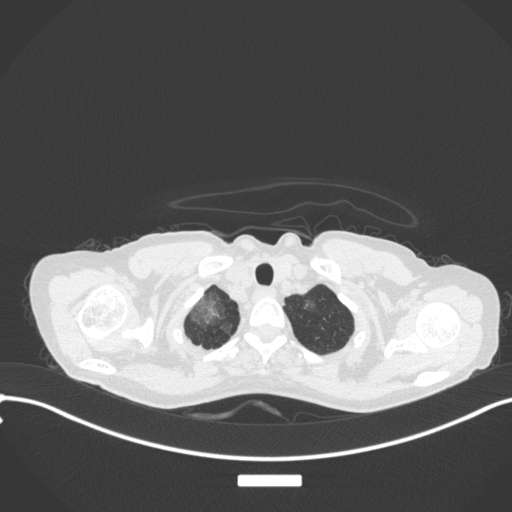
Chest CT, one axial slice. Slice 307 of 311 in the series (ordered by position). Reconstruction kernel B31f. 120 kVp. Lung window (W 1500 / L -600 HU). 512 × 512 image matrix, field of view 400 × 400 mm. Patient: female, 59 years. Case-level facts recorded for this patient, not image findings: clinical TNM (as recorded): T3 N0 M0; histopathological grade: G1.
Annotated regions visible in this slice (bounding box drawn by a radiologist):
- lung tumour (recorded histology: adenocarcinoma): bounding box (x1, y1, x2, y2) in pixels: (183, 294, 224, 328)